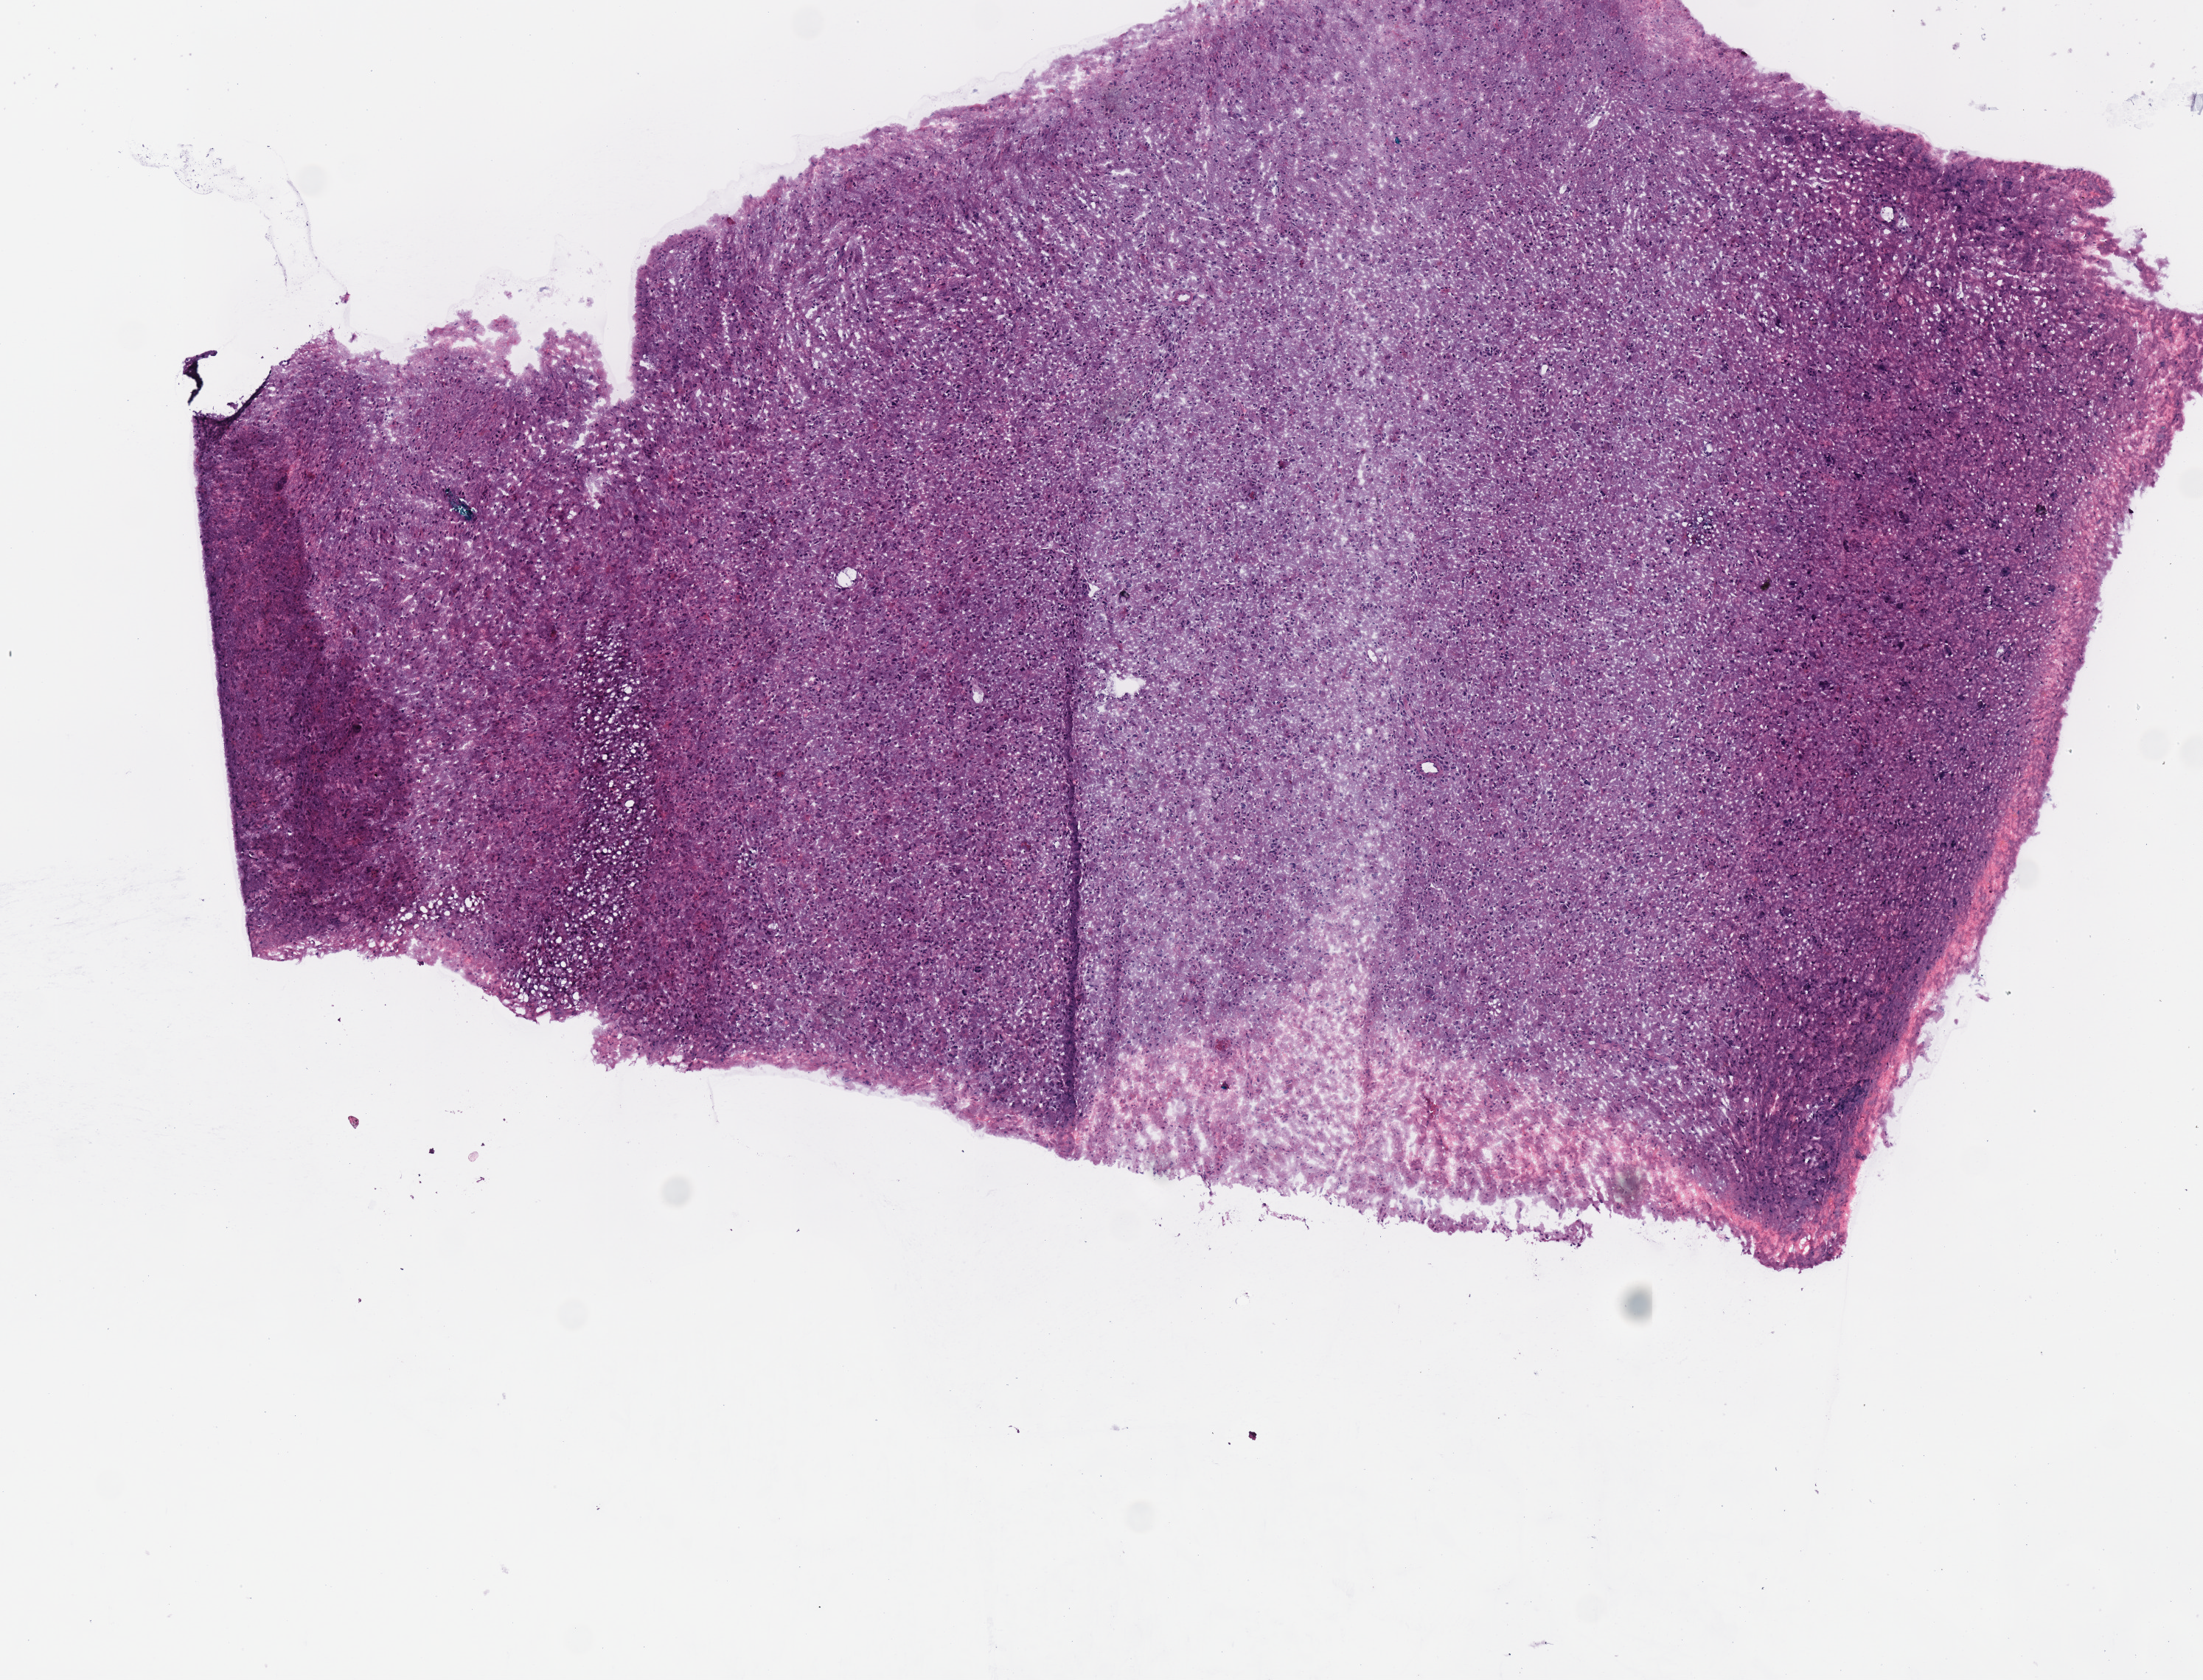
Whole-slide histology image, Hematoxylin and eosin (H&E) stained — low-resolution overview of the scanned area, about 5.9 x 4.5 mm; frozen section from the top of the tissue portion; sample: primary tumour, brain. Female, age 51 years at initial diagnosis. Histologic grade: G3 (poorly differentiated). Slide review estimates, as recorded: tumour cells 100%, tumour nuclei 70%, normal cells 0%, stromal cells 0%, necrosis 0%.
Diagnosis: Astrocytoma, anaplastic (cerebrum).